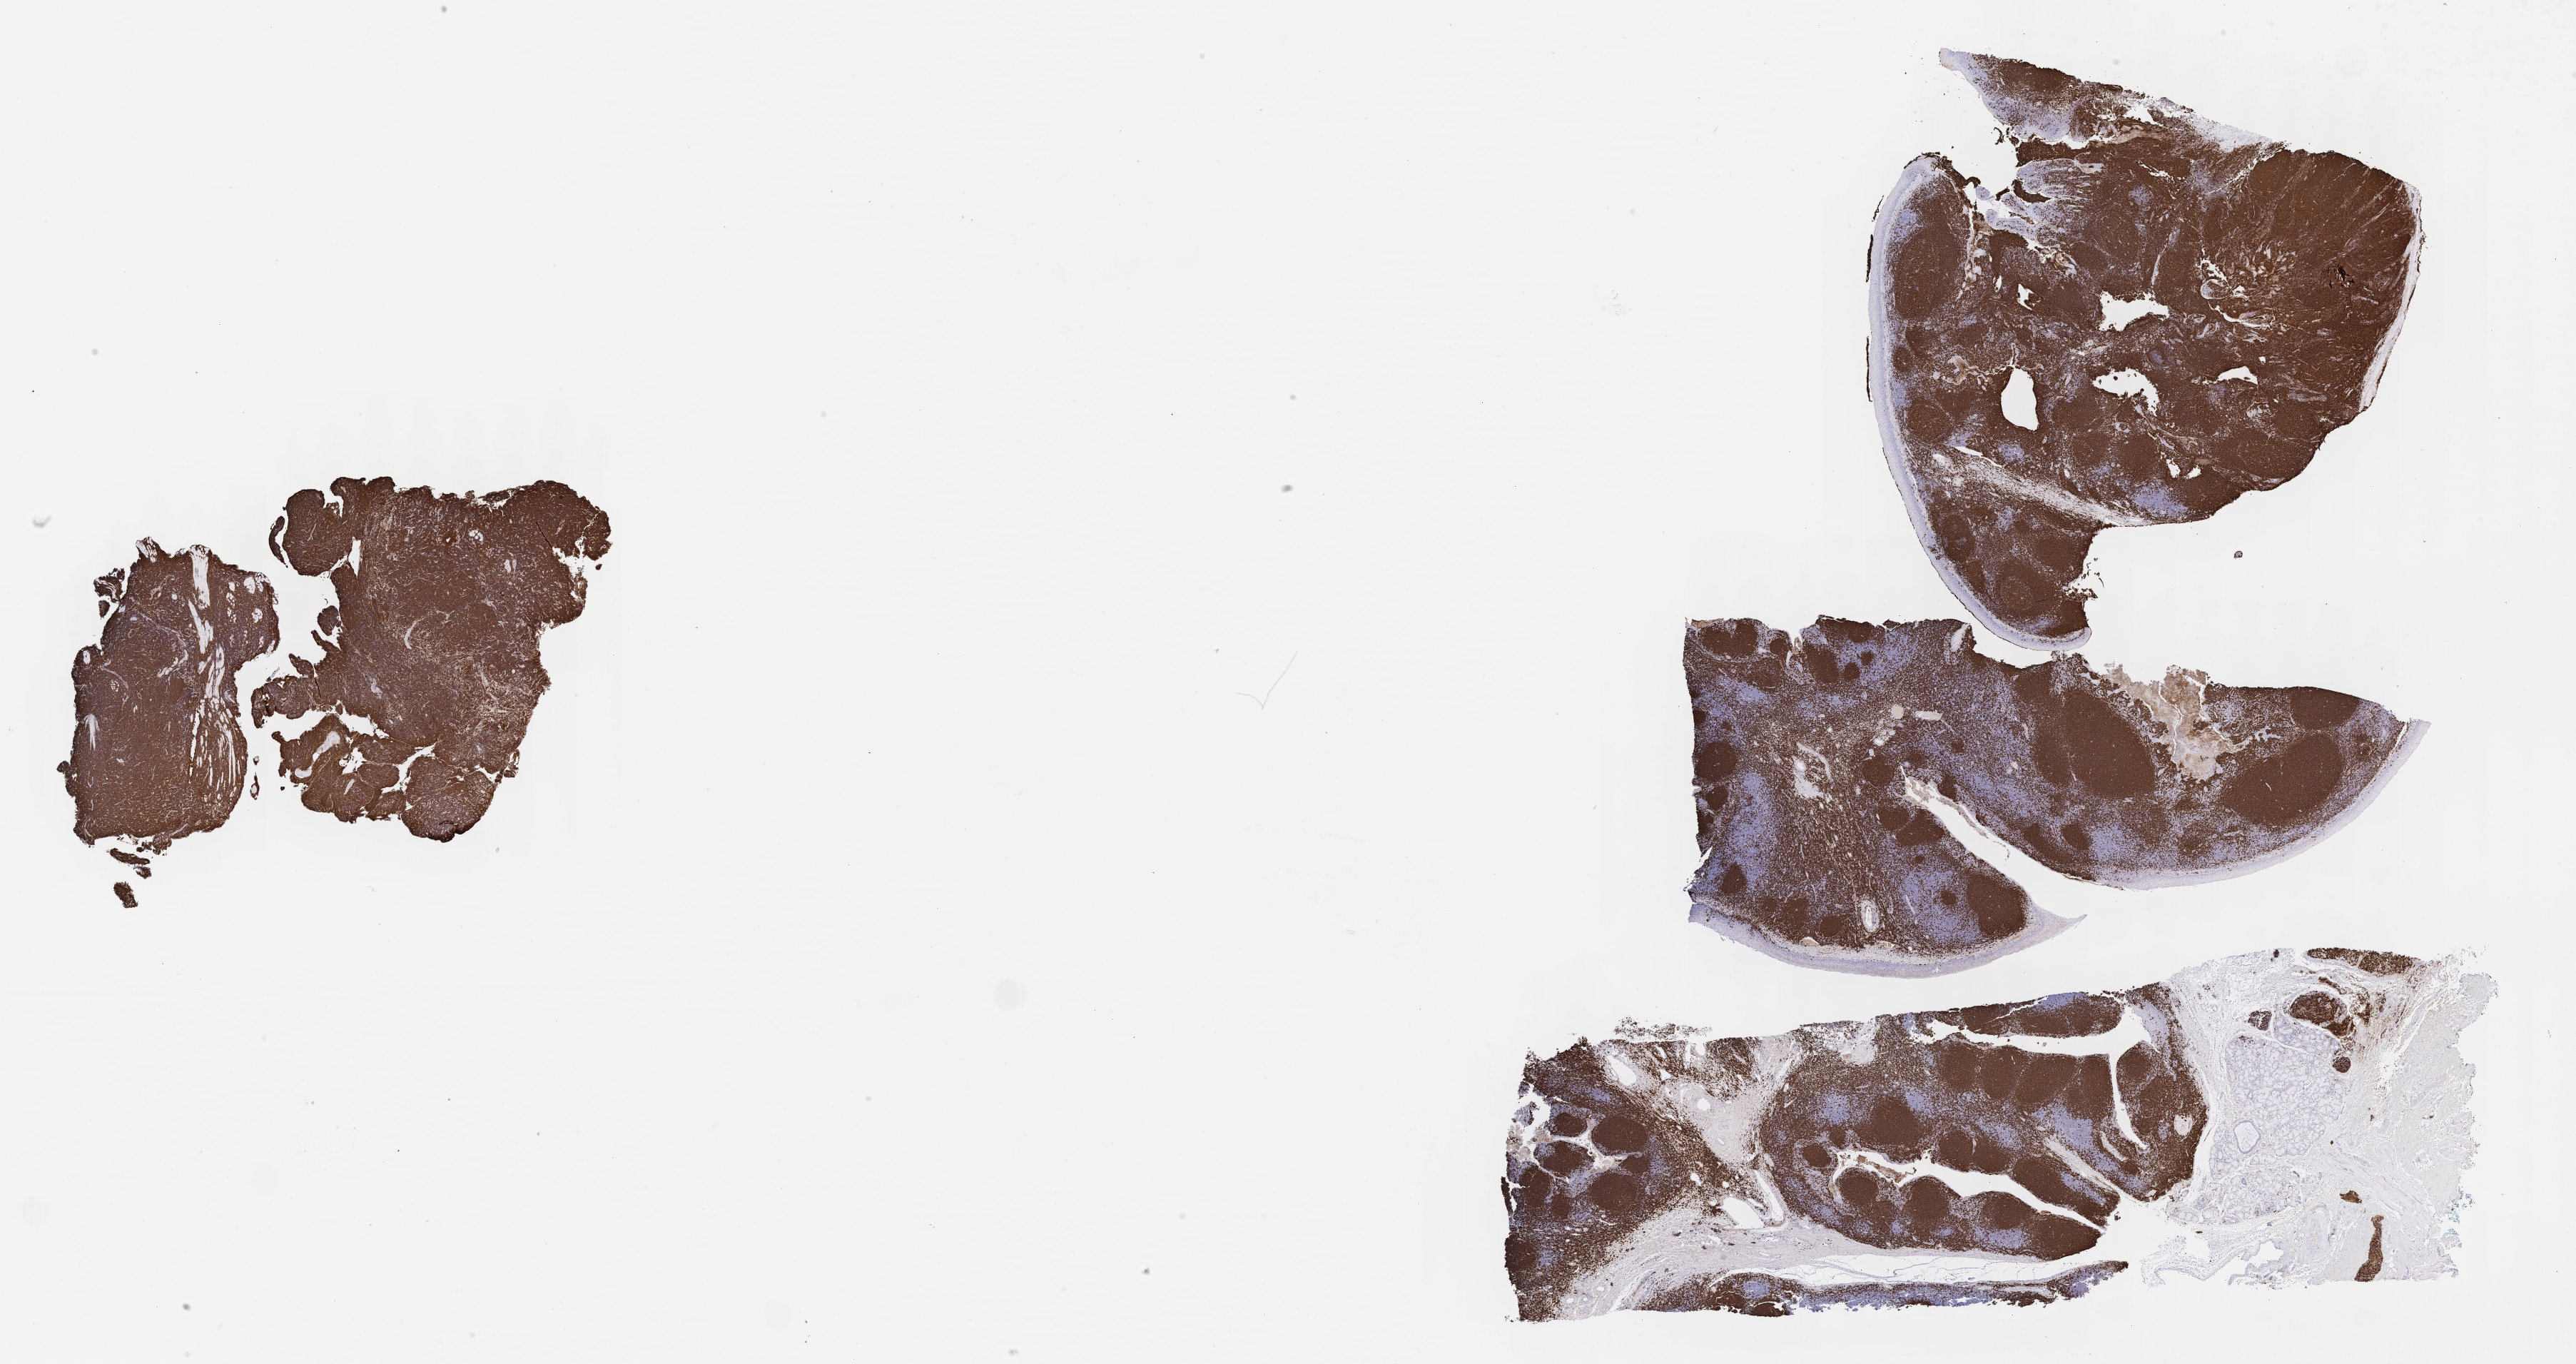
Whole-slide image, immunohistochemical stain for CD20 — shown as a low-resolution overview of the whole scanned area (about 29.2 x 15.4 mm), specimen: tumor tissue, site: cranium. Patient: male, age at initial diagnosis 8 years.
Diagnosis: Burkitt lymphoma, NOS.